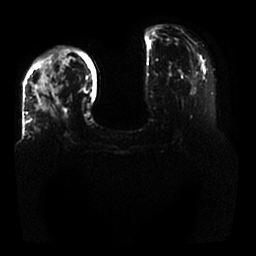
Breast MRI, one axial slice. Position 9 of 25 along the scan axis. Diffusion-weighted series; image 2 of 4 stored at this slice position (different b-values; order by instance number). 1.5 T. 4 mm slice thickness. 256 × 256 image matrix, field of view 350 × 350 mm. Female patient.
Structures marked on this image (outlined manually by an expert reader):
- tumour on diffusion-weighted imaging: bounding box [x1, y1, x2, y2] px = [36, 75, 61, 120]